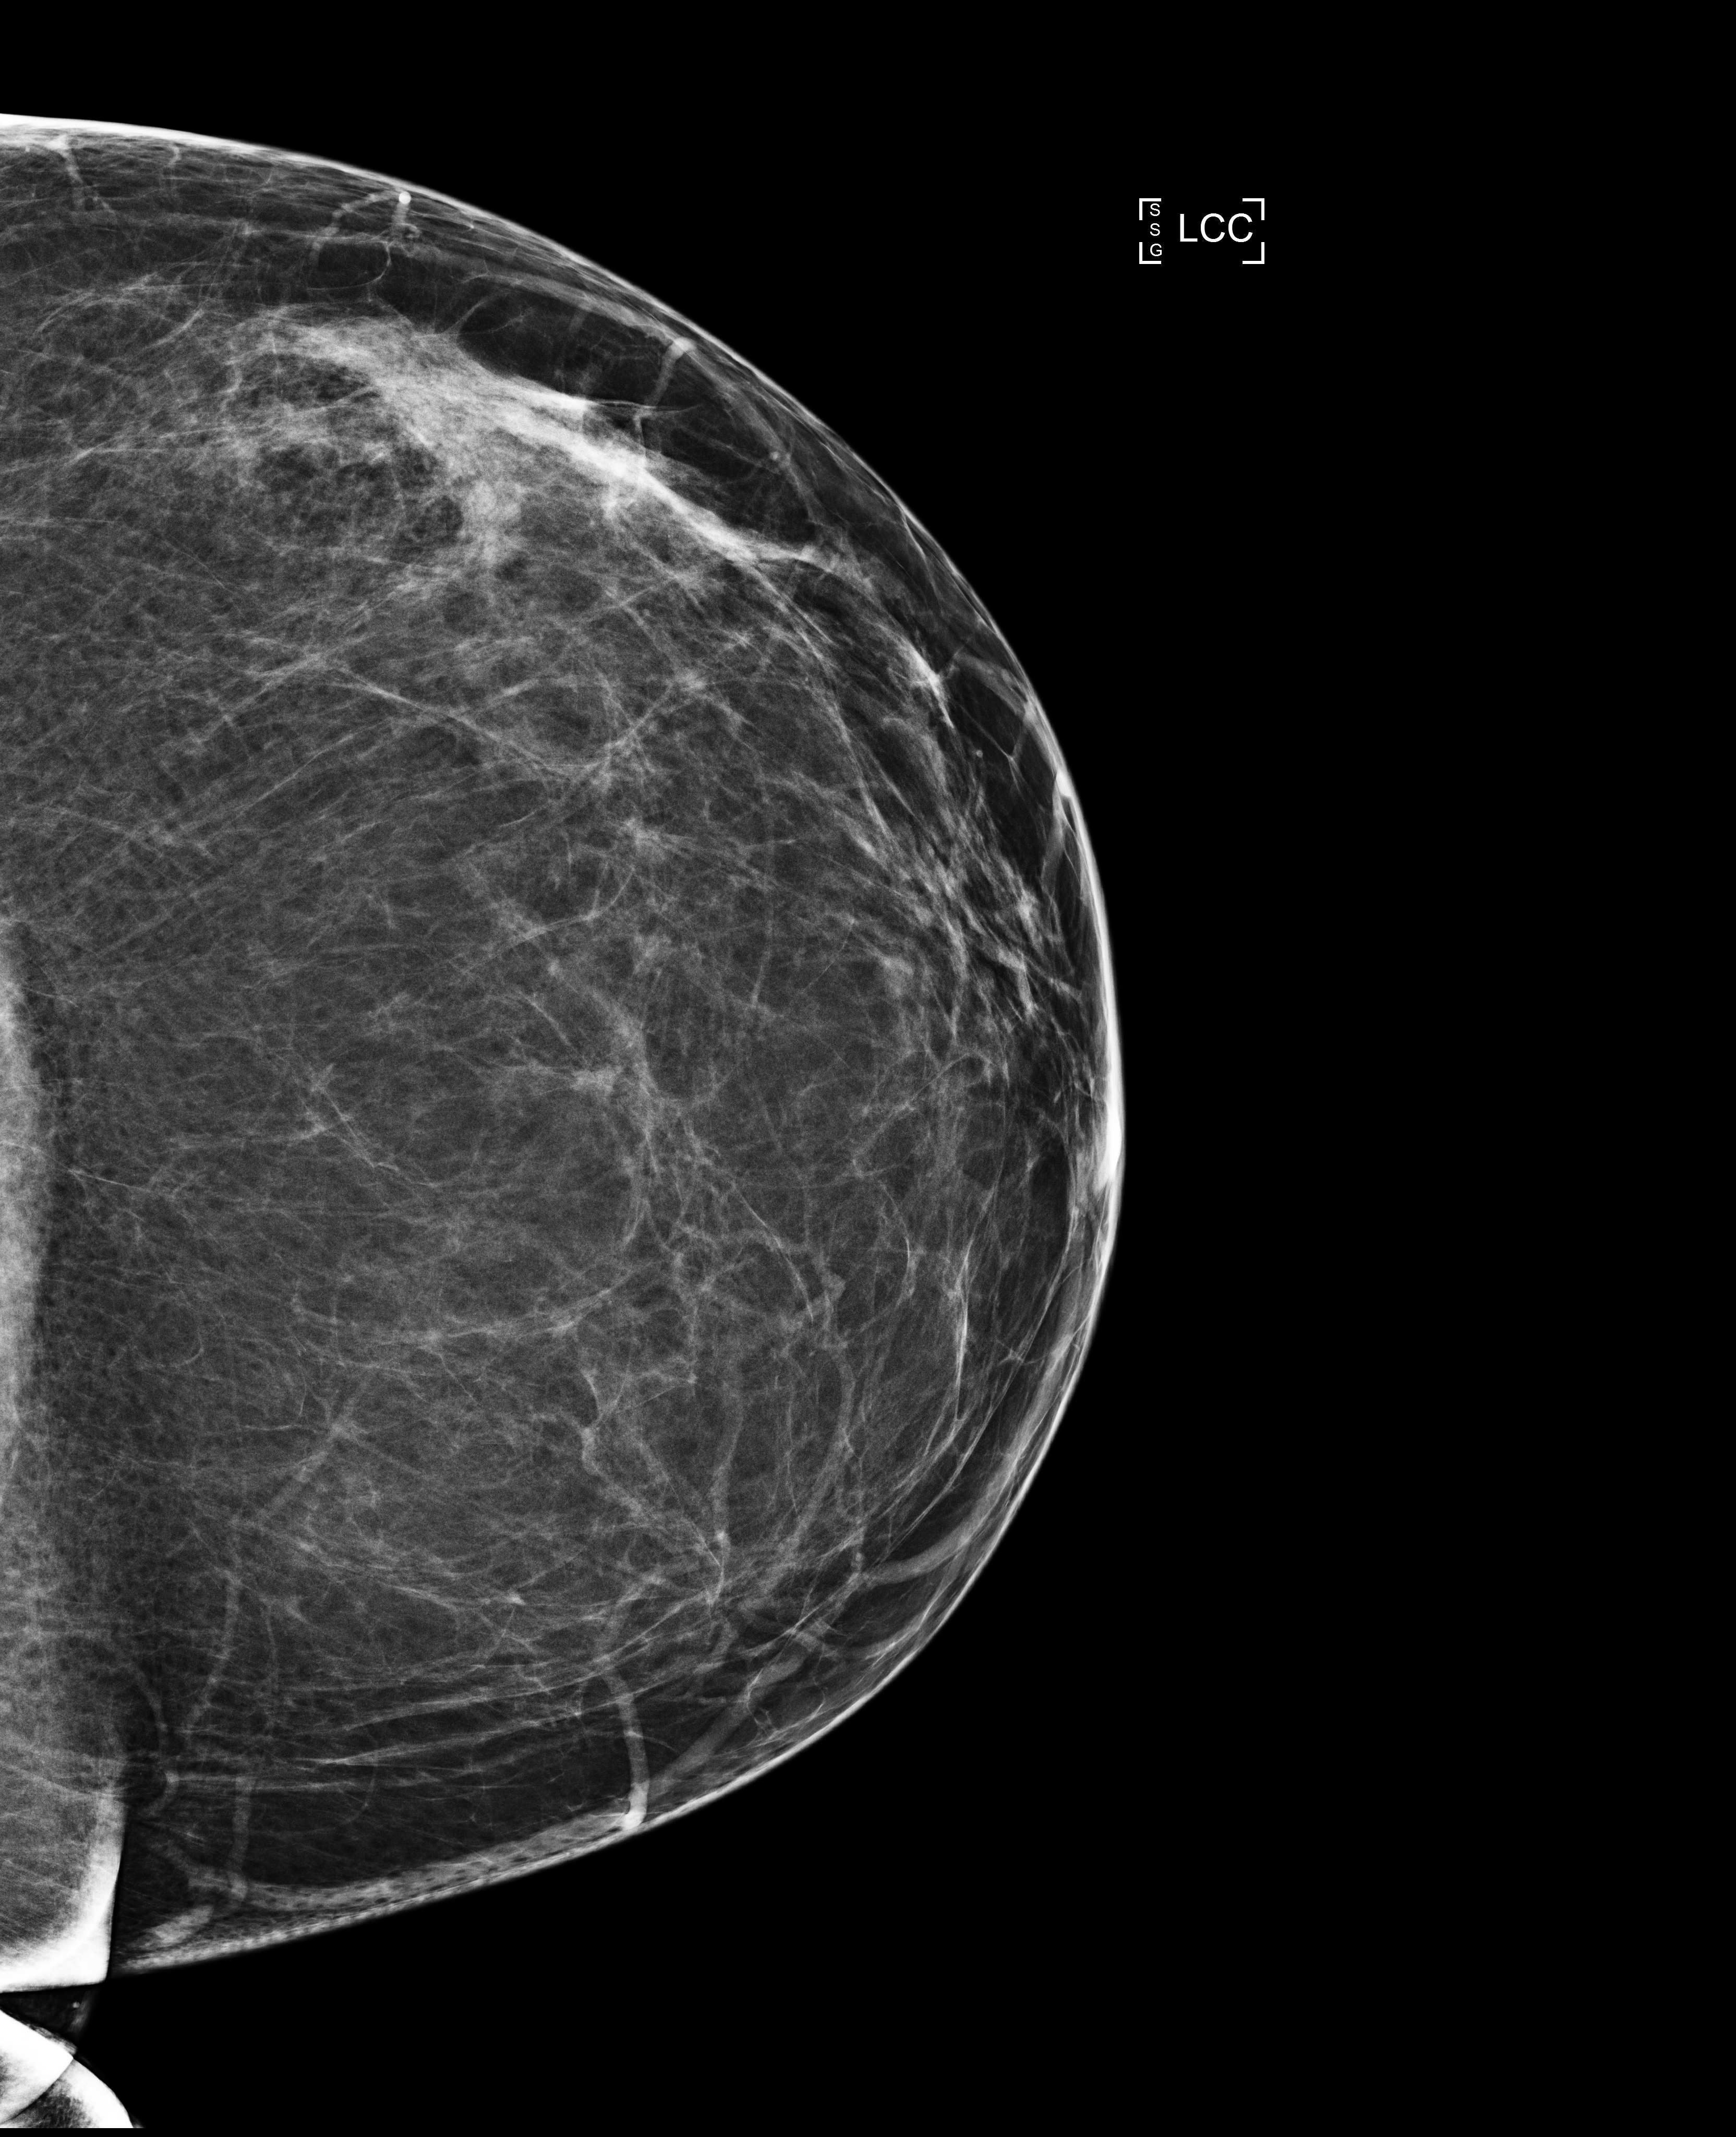
Digital mammogram (FFDM), left breast, craniocaudal (CC) view, annual screening mammography examination. Patient aged 51 years (female).
Final BI-RADS assessment for this screening round (tomosynthesis exam, both breasts): category 2.